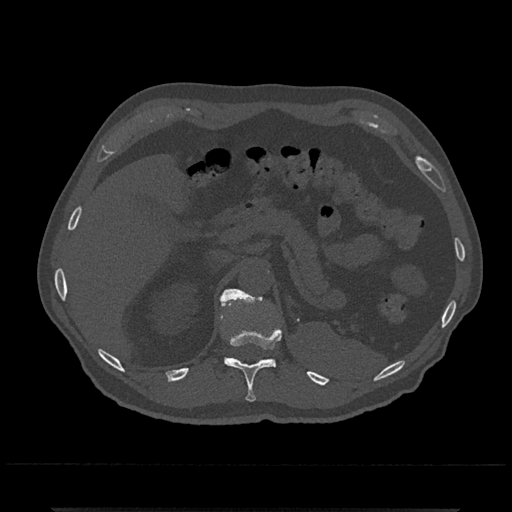
CT including the spine, one axial slice. Reconstruction kernel Br40s/3. 120 kVp. Bone window (W 1800 / L 400 HU). 512 × 512 image matrix, field of view 393 × 393 mm. Male patient, age 67 years. From the clinical record (not read from this slice): primary cancer: prostate.
Annotated regions visible in this slice (semi-automatically segmented with operator editing):
- T11 vertebra: bounding box [x1, y1, x2, y2] px = [221, 299, 282, 402]
- T12 vertebra: [221, 289, 264, 358]